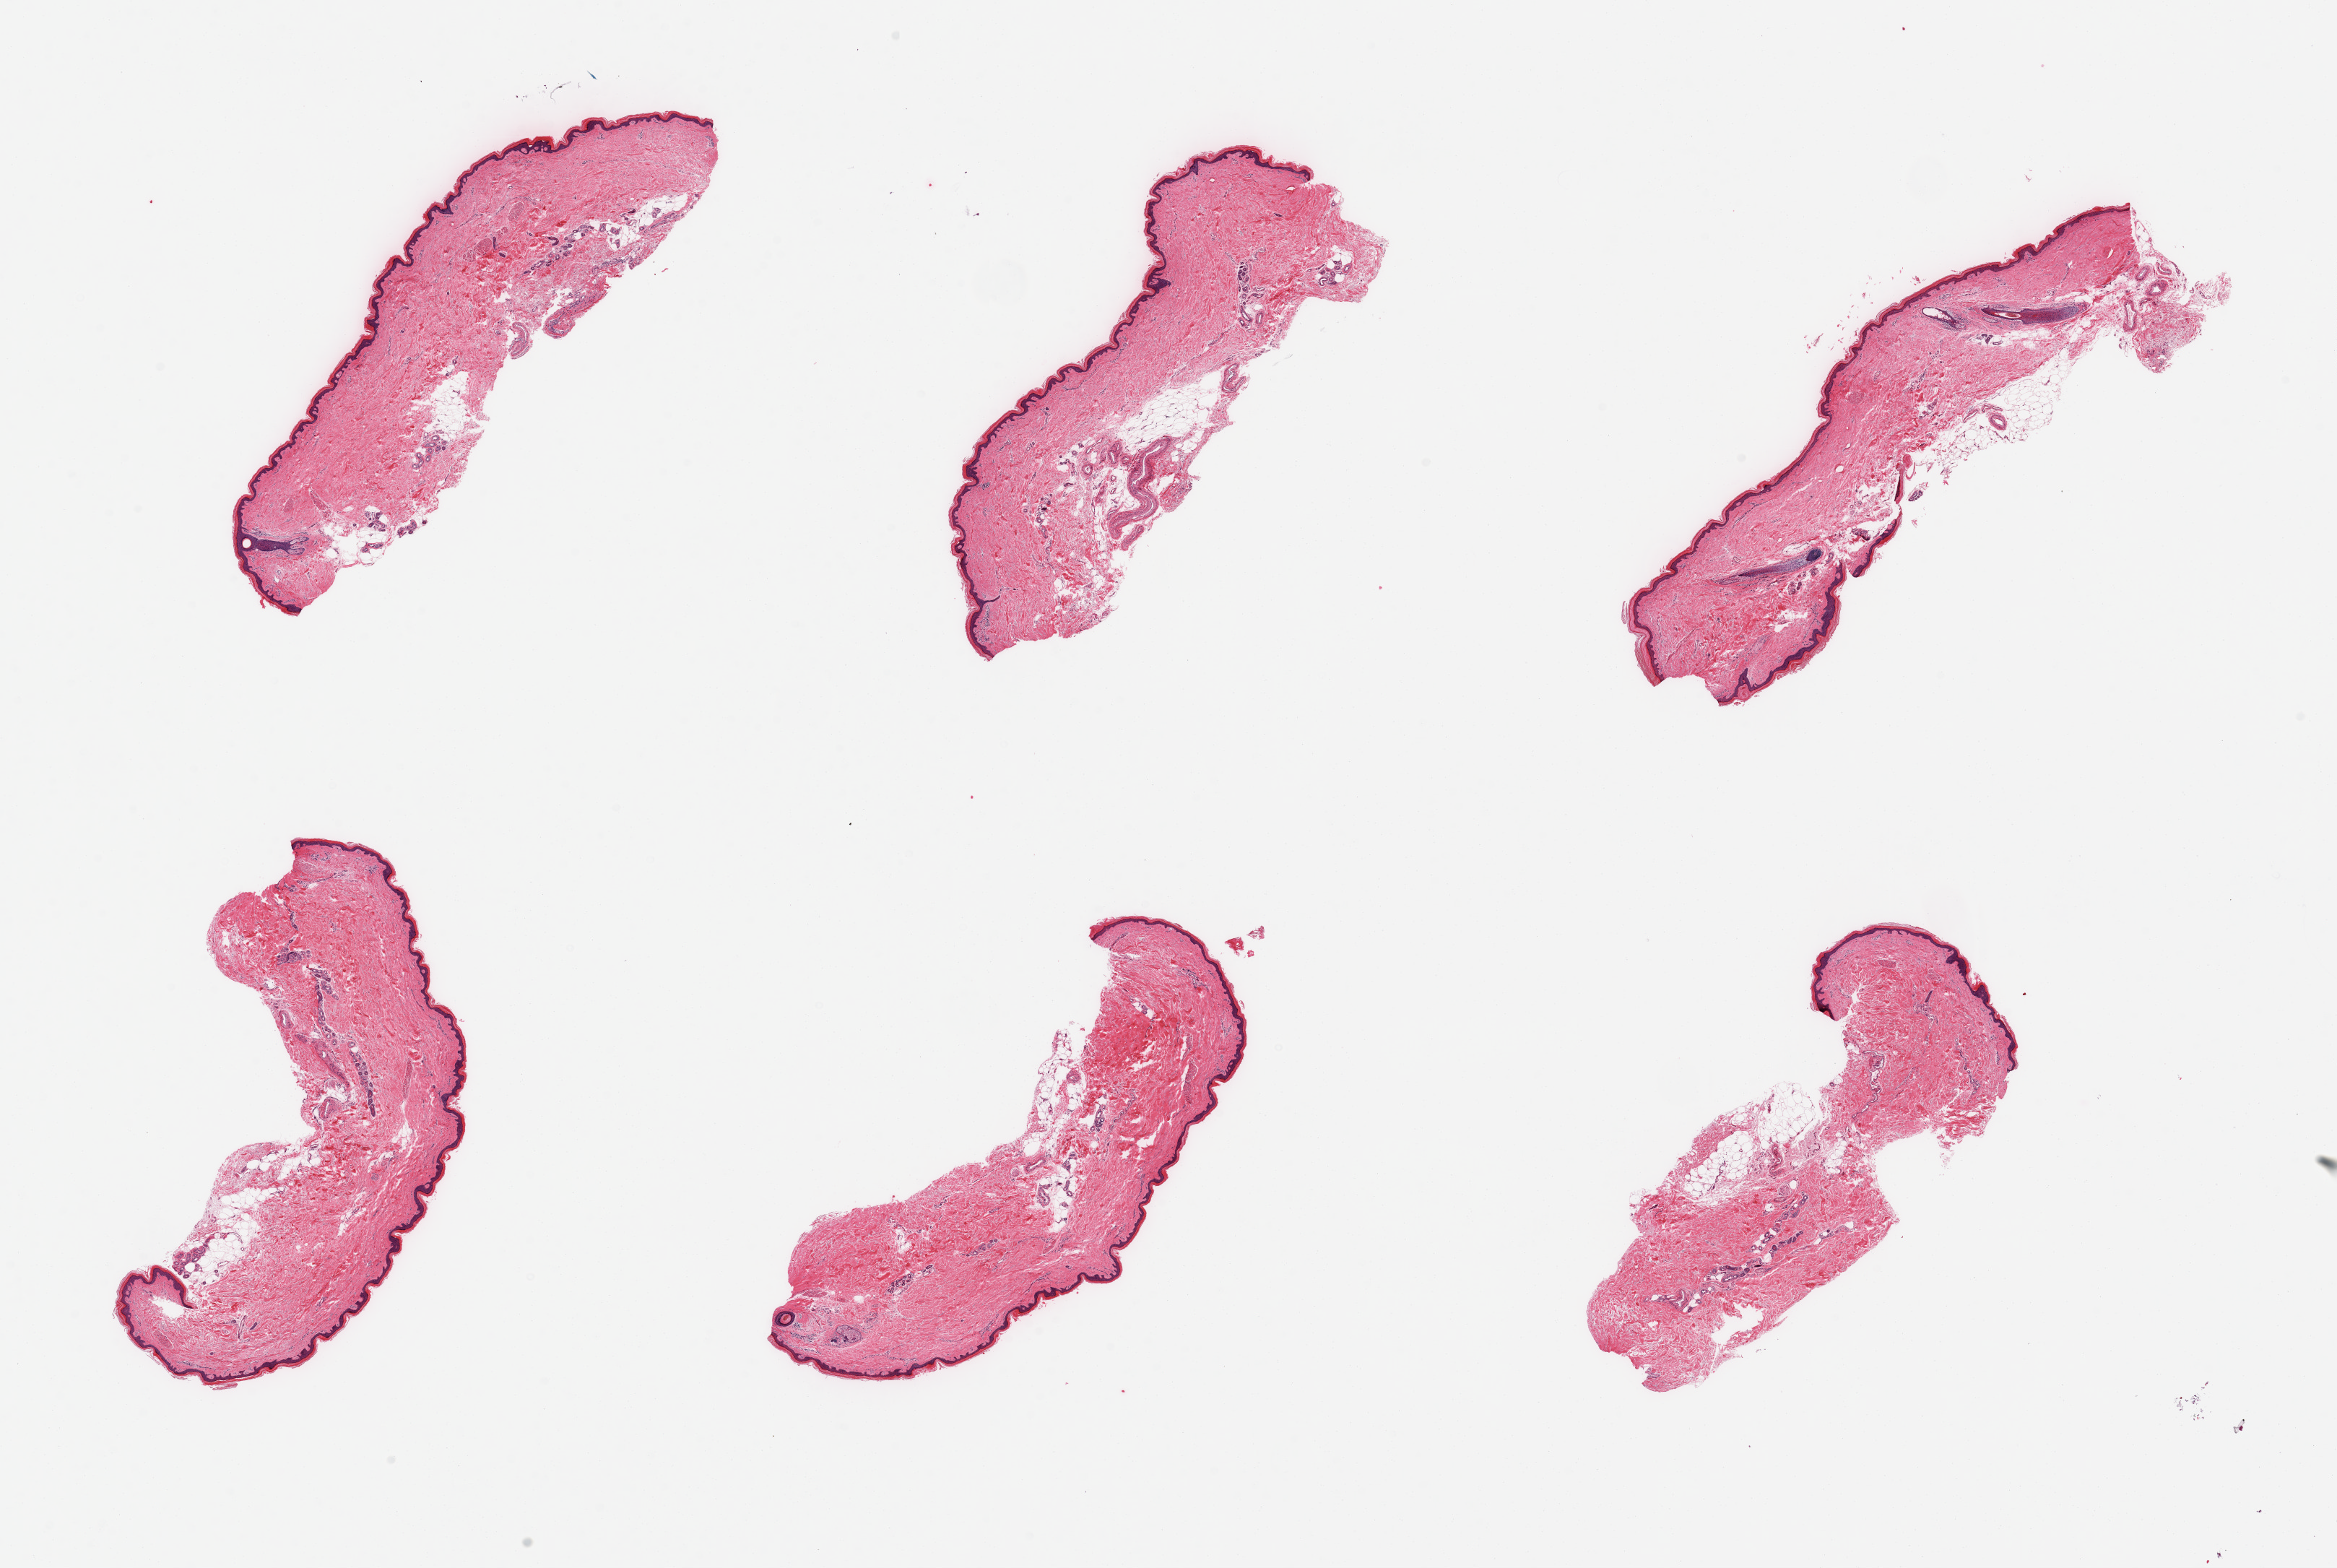
Whole-slide image, hematoxylin and eosin (H&E) stain, a low-resolution overview of the entire scanned area, about 25.6 x 17.2 mm (slide scanned at 20x), PAXgene-fixed paraffin-embedded (PFPE) section, section of skin of lower leg (target tissue), donor tissue sample. Donor: female.
Pathologist's review note for this sample: 6 pieces; up to ~10% fat, largely external, epidermis measures 41 microns.